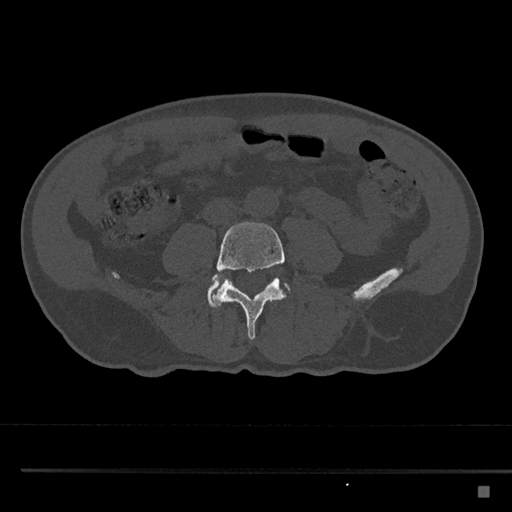
CT including the spine, one axial slice; slice 630 of 797 in the series (ordered by position); reconstruction kernel Br40s/3; bone window (W 1800 / L 400 HU); 512 × 512 image matrix, field of view 391 × 391 mm. Male patient, age 59 years. Case-level facts recorded for this patient, not image findings: primary cancer: prostate.
Structures marked on this image (semi-automatically segmented with operator editing):
- L4 vertebra: bounding box (x1, y1, x2, y2) in pixels: (212, 221, 289, 340)
- L5 vertebra: (207, 275, 291, 309)